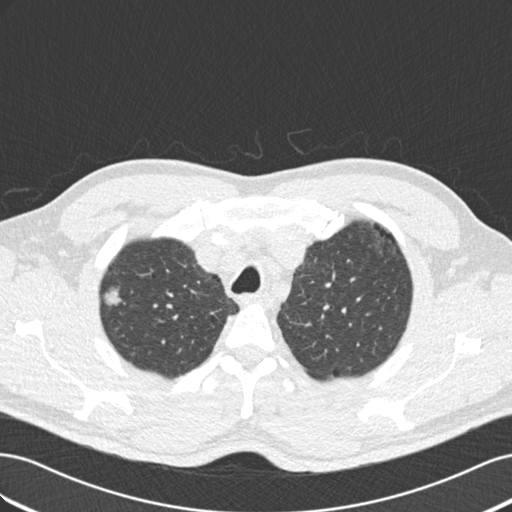
Chest CT (low-dose screening protocol), one axial image, second annual screen, lung window (W 1500 / L -600 HU), 2 mm slice thickness, standard (soft-tissue) reconstruction kernel (B30f), 120 kVp, 512 × 512 image matrix, field of view 360 × 360 mm. Male, age 56 years at enrolment. Current smoker at enrolment.
Lesion marked by an expert reader, box from (x=86, y=281) to (x=131, y=317) px. Reader record for this screening exam (exam-level; its link to the box is not recorded): non-calcified nodule or mass ≥4 mm, right upper lobe, 13 × 12 mm, smooth margins, mixed attenuation, pre-existing on the prior screen: yes; interval growth: yes. Official screen result: positive, change unspecified: nodule(s) >= 4 mm or enlarging nodule(s), mass(es), or other non-specific abnormalities suspicious for lung cancer. Lung cancer was diagnosed 174 days after this screen: bronchiolo-alveolar carcinoma, non-mucinous, right upper lobe, moderately differentiated (G2), stage IIIB (AJCC 6th edition), 10 mm at pathology.